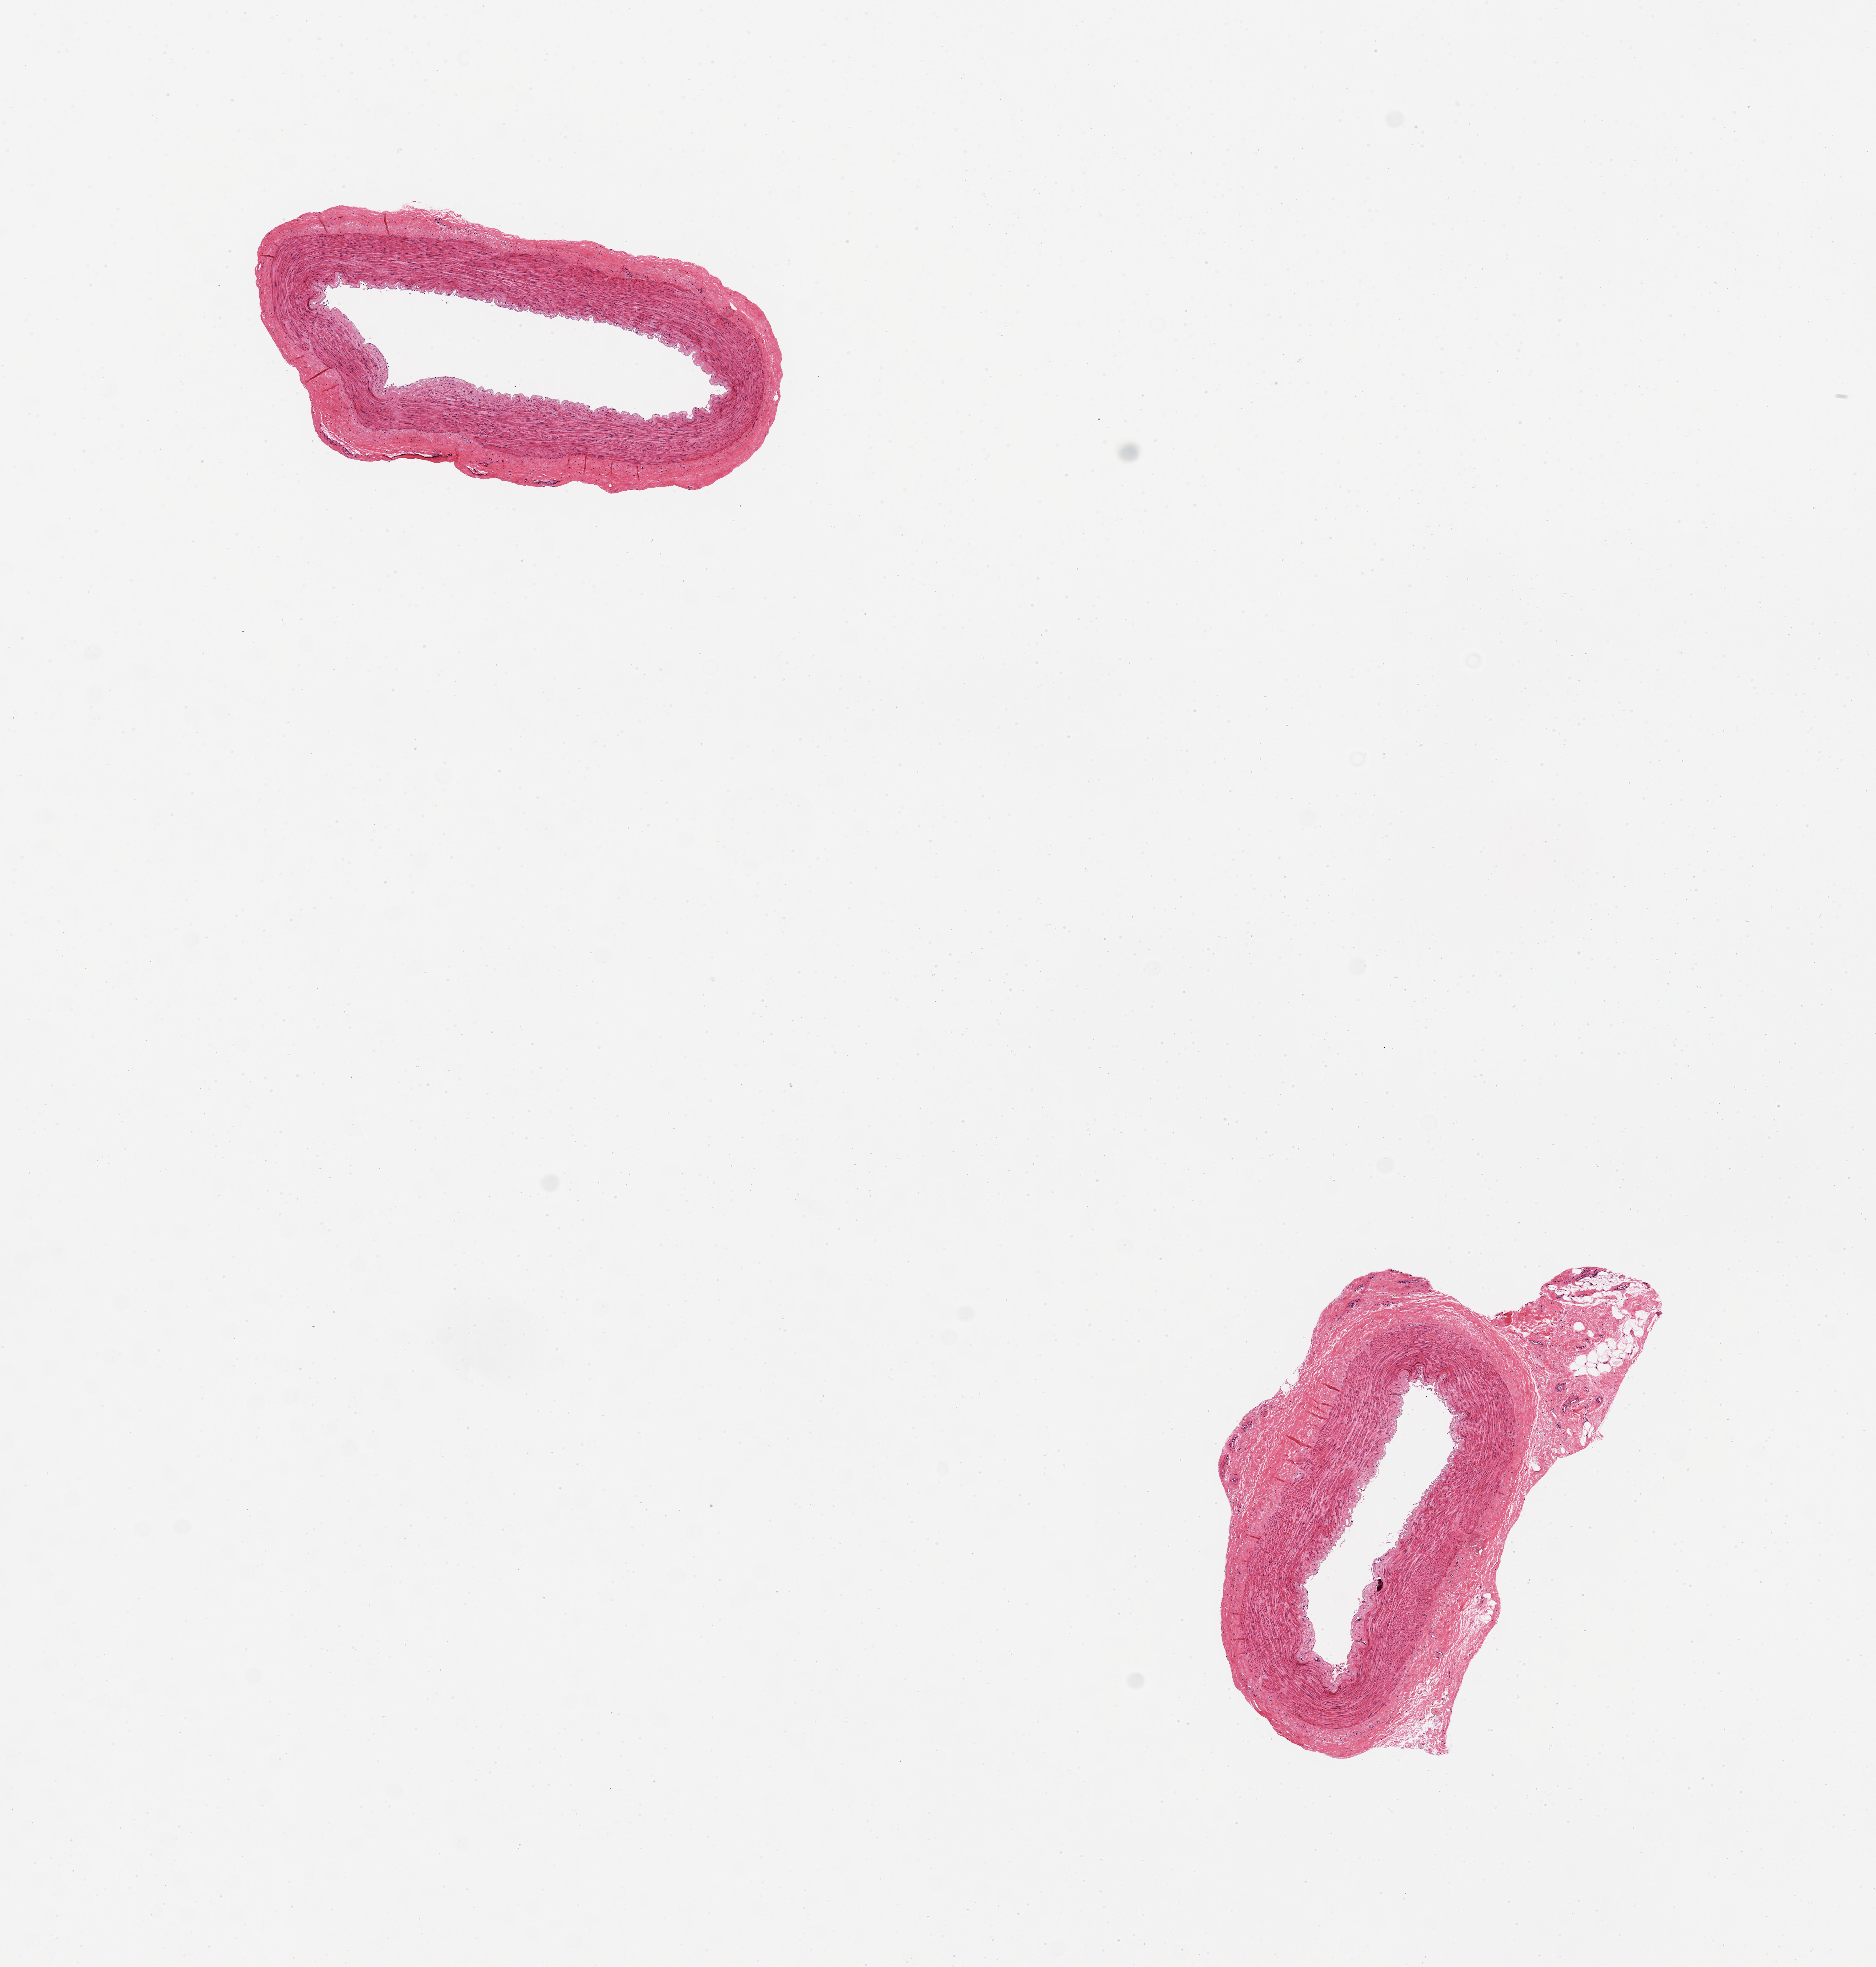
Haematoxylin and eosin whole-slide image, a low-resolution overview of the entire scanned area, about 11.8 x 12.4 mm. PAXgene-fixed paraffin-embedded (PFPE) section. Target tissue: tibial artery. Donor tissue sample. Donor sex: male.
Pathologist's review note for this sample: 2 pieces, few foci of calcification, small attachment of fibrofatty tissue.